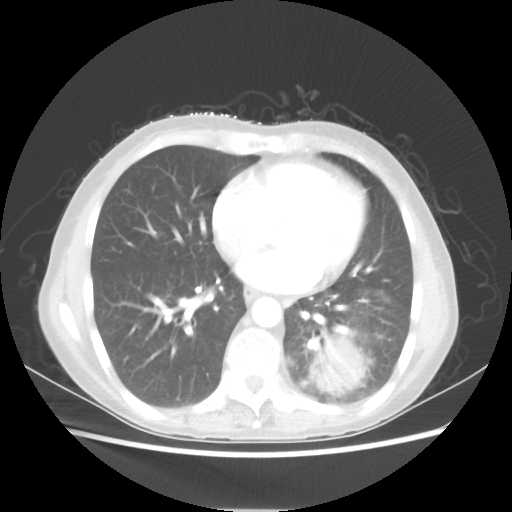
Chest CT, one axial slice; slice 22 of 56 in the series (ordered by position); 80 kVp; lung window (W 1500 / L -600 HU); 512 × 512 image matrix, field of view 360 × 360 mm. Female patient, age 53 years. From the clinical record (not read from this slice): clinical TNM (as recorded): T3 N0 M0.
Outlined on this slice (rectangle marked by the reading radiologist):
- lung tumour (recorded histology: adenocarcinoma): bounding box [x1, y1, x2, y2] px = [307, 333, 367, 396]